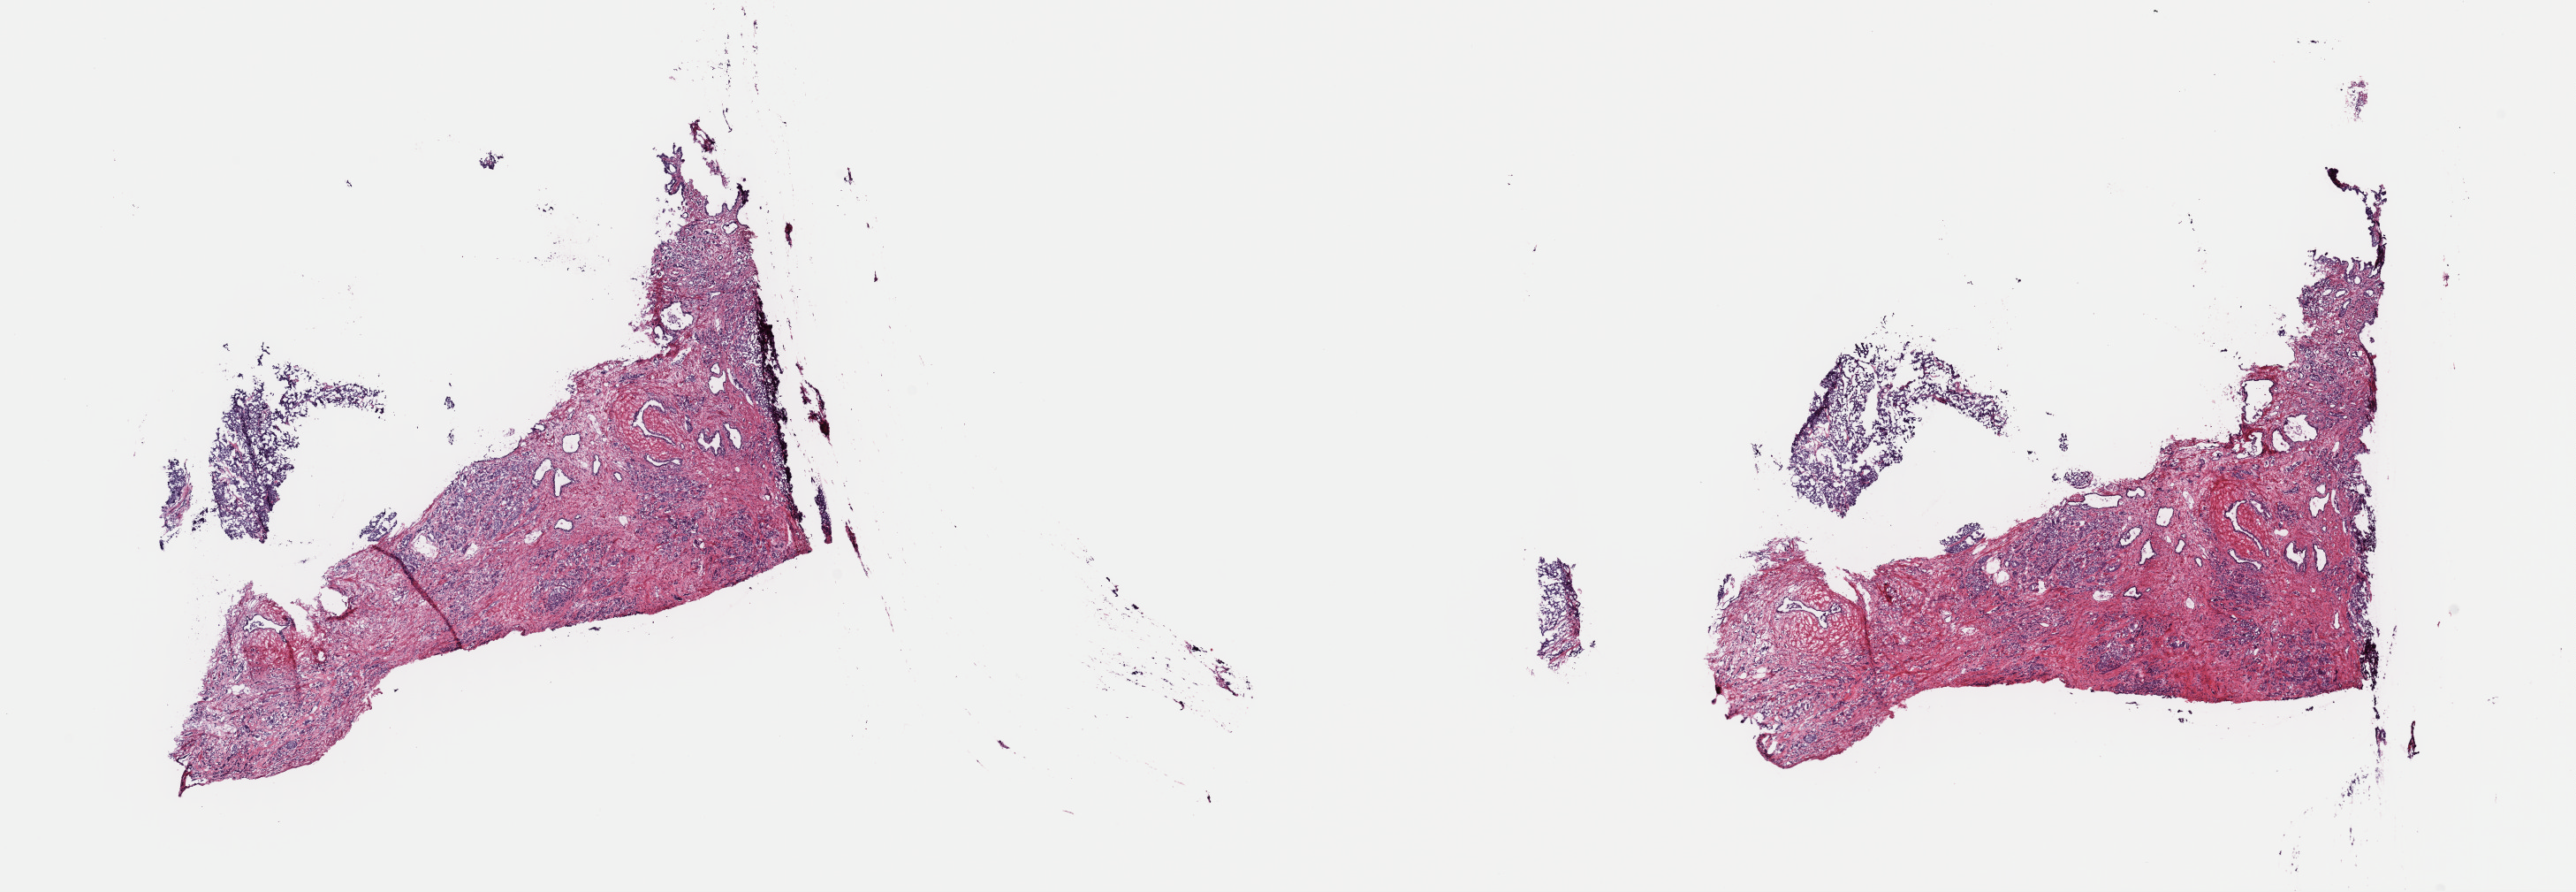
Digitized Hematoxylin and eosin (H&E) stained tissue section (whole slide), low-resolution overview of the scanned area, about 23.0 x 8.0 mm (slide scanned at 40x), frozen section from the top of the tissue portion, prostate, primary tumour sample. Patient: male, age at initial diagnosis 55 years. Gleason score: 9 (4+5). Slide review estimates, as recorded: tumour cells 65%, tumour nuclei 65%, normal cells 10%, stromal cells 25%, necrosis 0%. Infiltration values recorded for this section: lymphocyte infiltration 3%, monocyte infiltration 0%, neutrophil infiltration 0%.
Laterality: right. Diagnosis: Adenocarcinoma, NOS (prostate gland). Lymph nodes positive (case pathology): 2 of 15 examined.